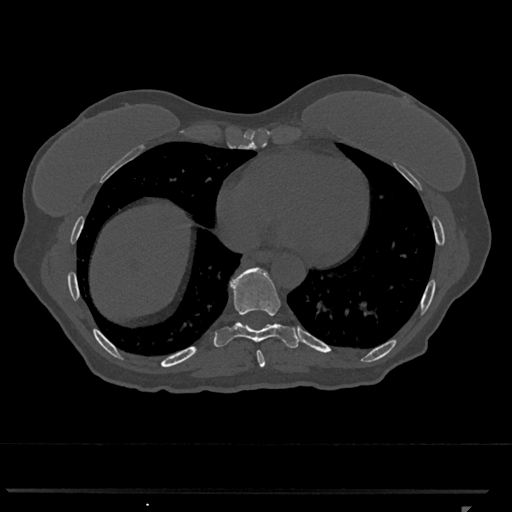
CT including the spine, one axial slice; slice 619 of 793 in the series (ordered by position); reconstruction kernel Br40s/3; 120 kVp; bone window (W 1800 / L 400 HU); 0.5 mm slice thickness; 512 × 512 image matrix, field of view 380 × 380 mm. Patient: female, 62 years. Case-level facts recorded for this patient, not image findings: primary cancer: renal.
Outlined on this slice (semi-automatically segmented with operator editing):
- T8 vertebra: bounding box <256,350,265,367> (left, top, right, bottom; pixels)
- T9 vertebra: <214,267,300,348>